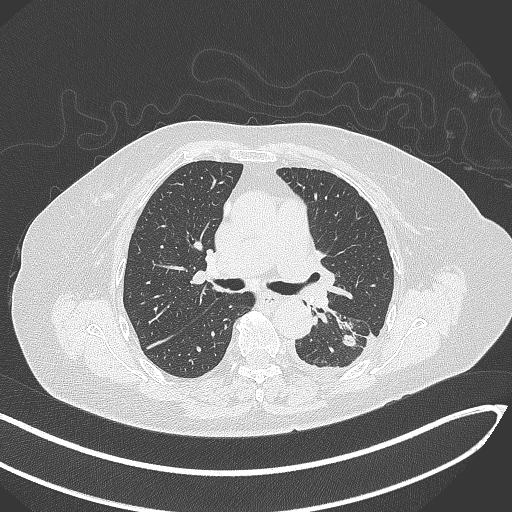
Chest CT, one axial slice; slice 191 of 270 in the series (ordered by position); 120 kVp; lung window (W 1500 / L -600 HU); 1 mm slice thickness; 512 × 512 image matrix, field of view 400 × 400 mm. Patient: female, 76 years. Case-level facts recorded for this patient, not image findings: clinical TNM (as recorded): T1c N0 M0.
Outlined on this slice (bounding box drawn by a radiologist):
- lung tumour (recorded histology: adenocarcinoma): box from (x=336, y=323) to (x=359, y=349) px